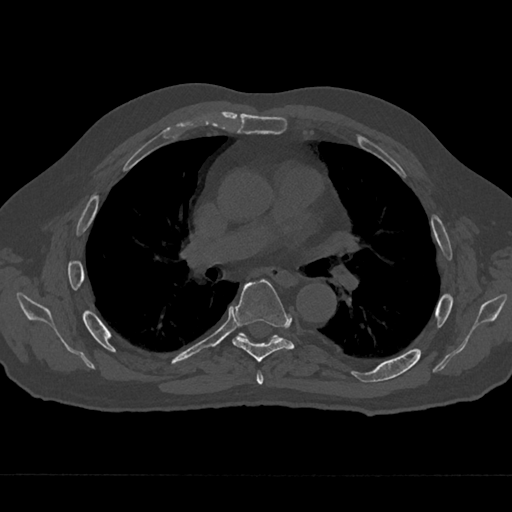
CT including the spine, one axial slice. Slice 416 of 797 in the series (ordered by position). Reconstruction kernel Br40s/3. 120 kVp. Bone window (W 1800 / L 400 HU). 512 × 512 image matrix, field of view 377 × 377 mm. Male patient, age 75 years. Case-level facts recorded for this patient, not image findings: primary cancer: renal.
Structures marked on this image (semi-automatic segmentation, software-assisted and operator-edited):
- T5 vertebra: bounding box <256,371,264,385> (left, top, right, bottom; pixels)
- T6 vertebra: <232,279,295,362>
- T7 vertebra: <241,334,277,339>